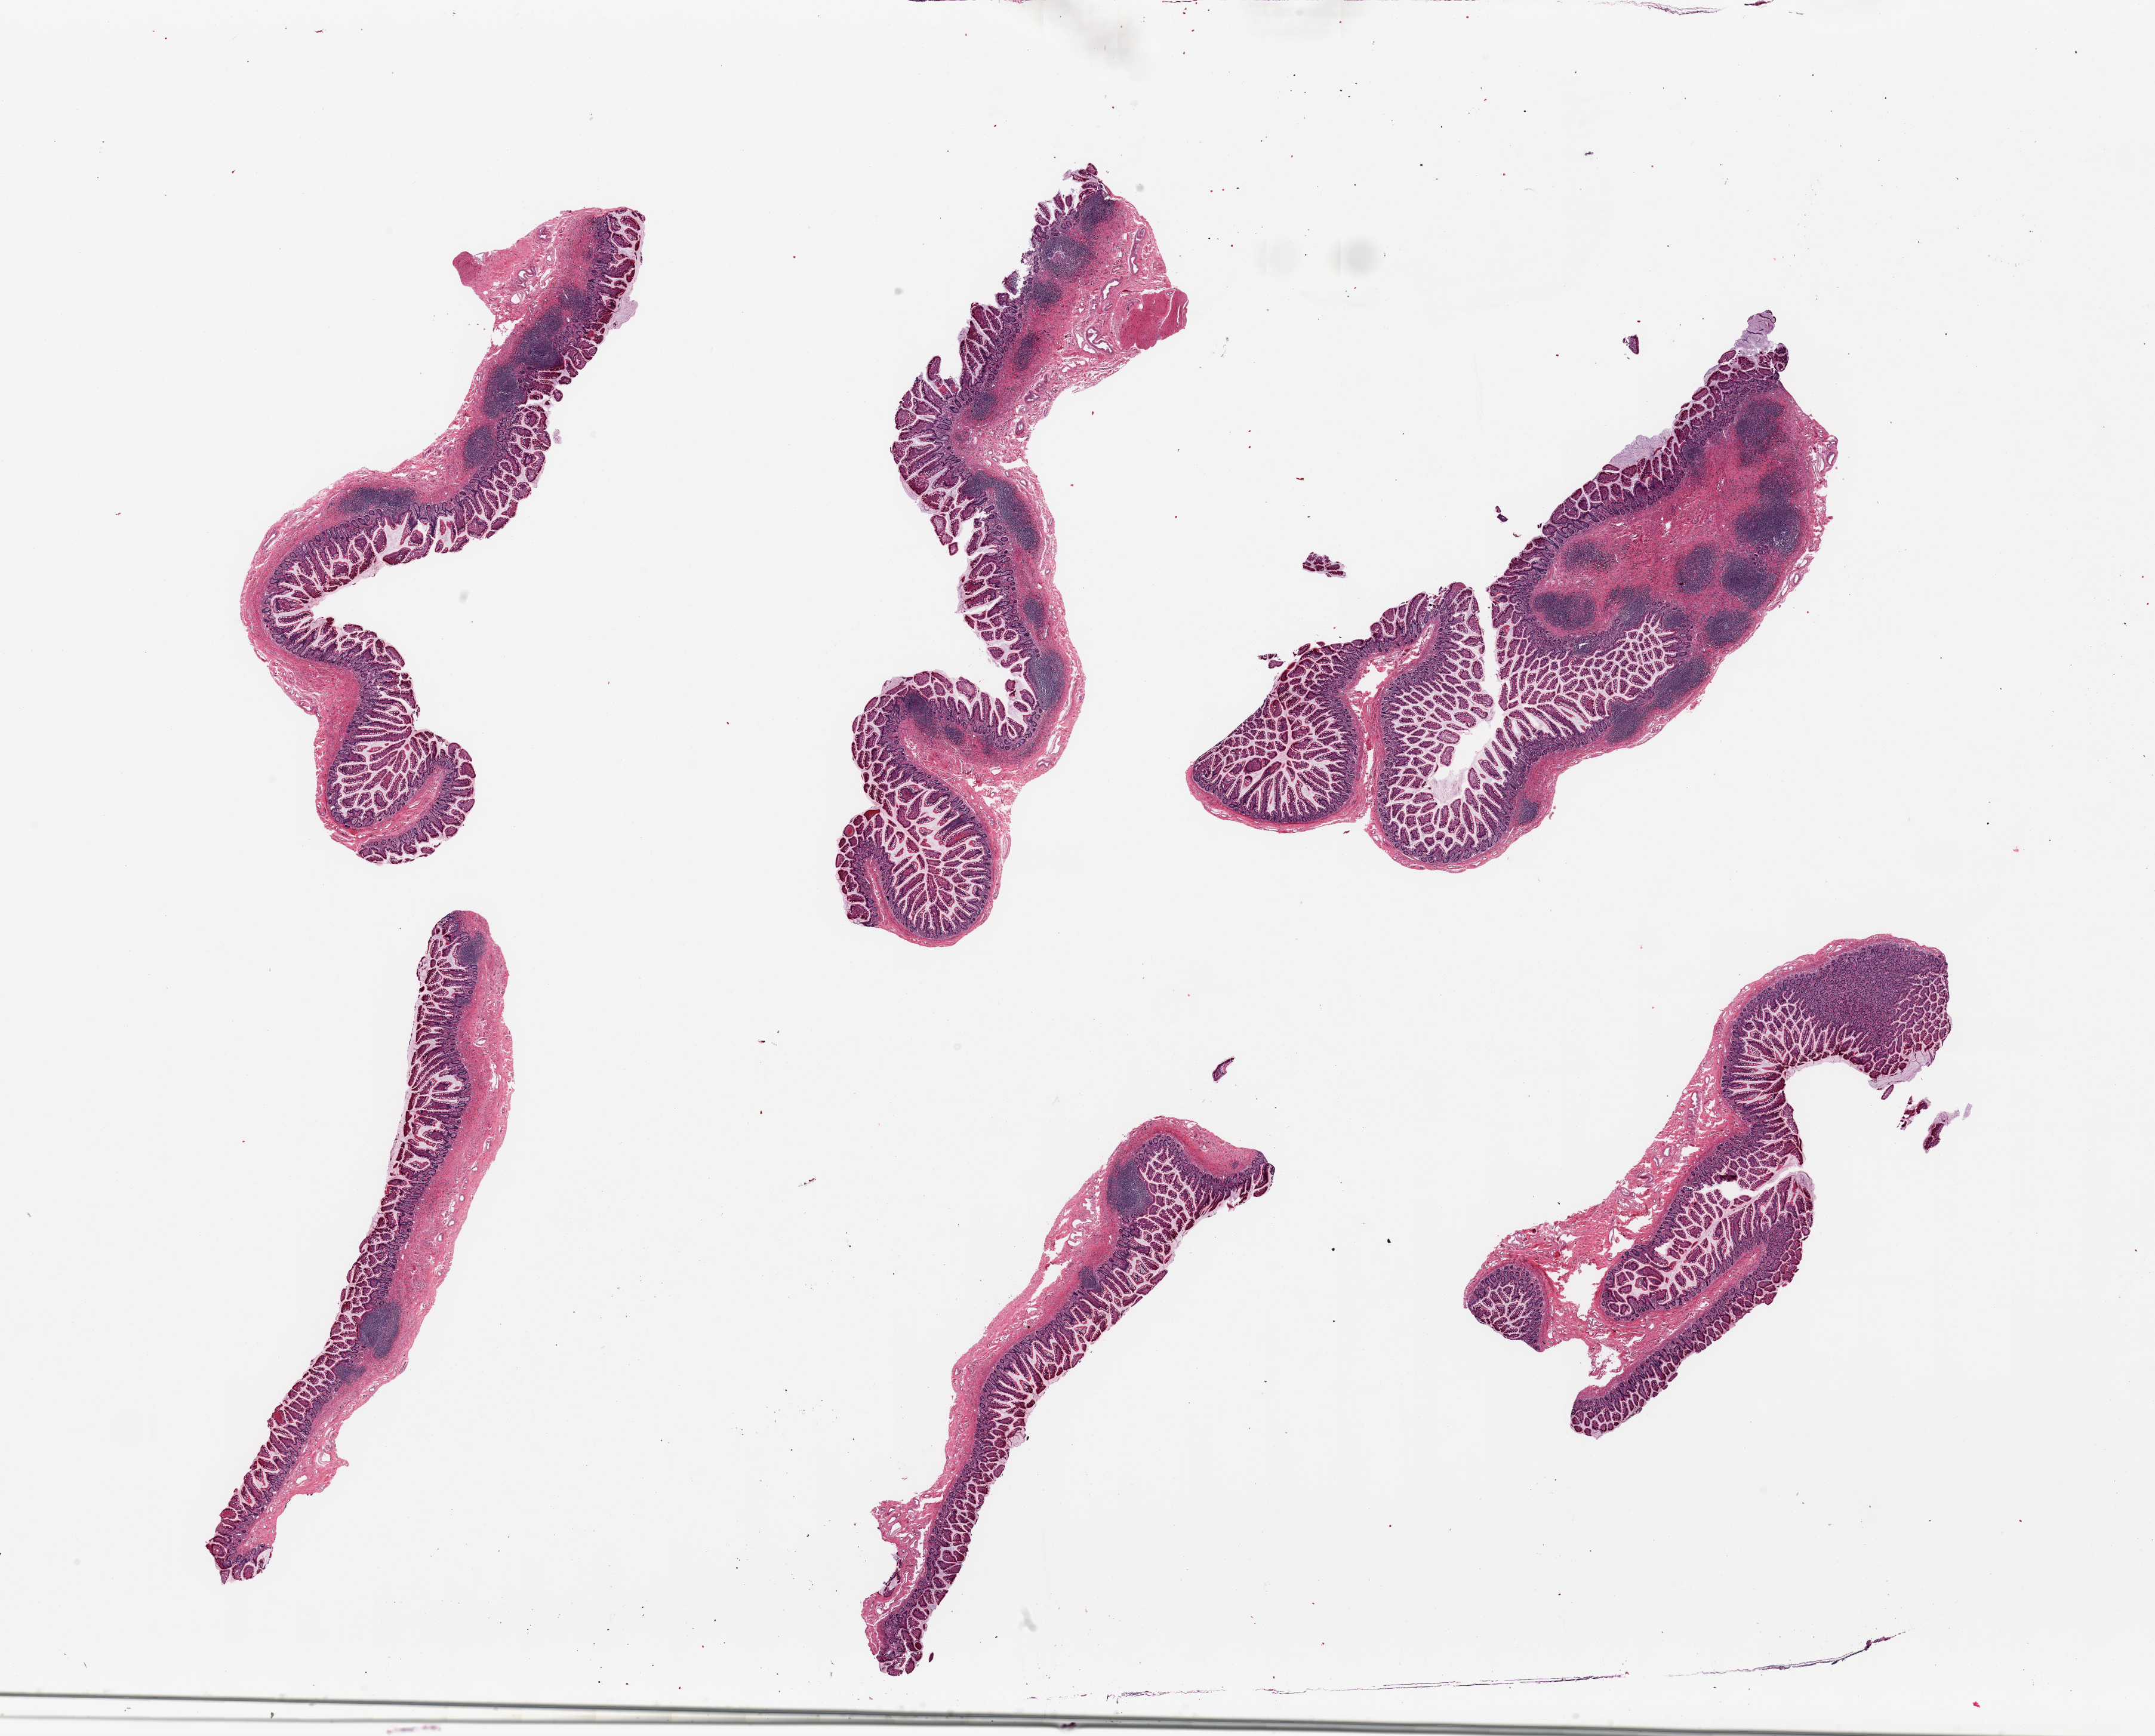
Hematoxylin and eosin (H&E) whole-slide image, brightfield — shown as a low-resolution overview of the whole scanned area (about 28.5 x 23.0 mm), PAXgene-fixed paraffin-embedded (PFPE) section, sampled site (target tissue): ileum, tissue donor sample. Donor: male.
• reviewer comment on this tissue sample: 6 pieces; well preserved mucosa and numerous lymphoid nodules